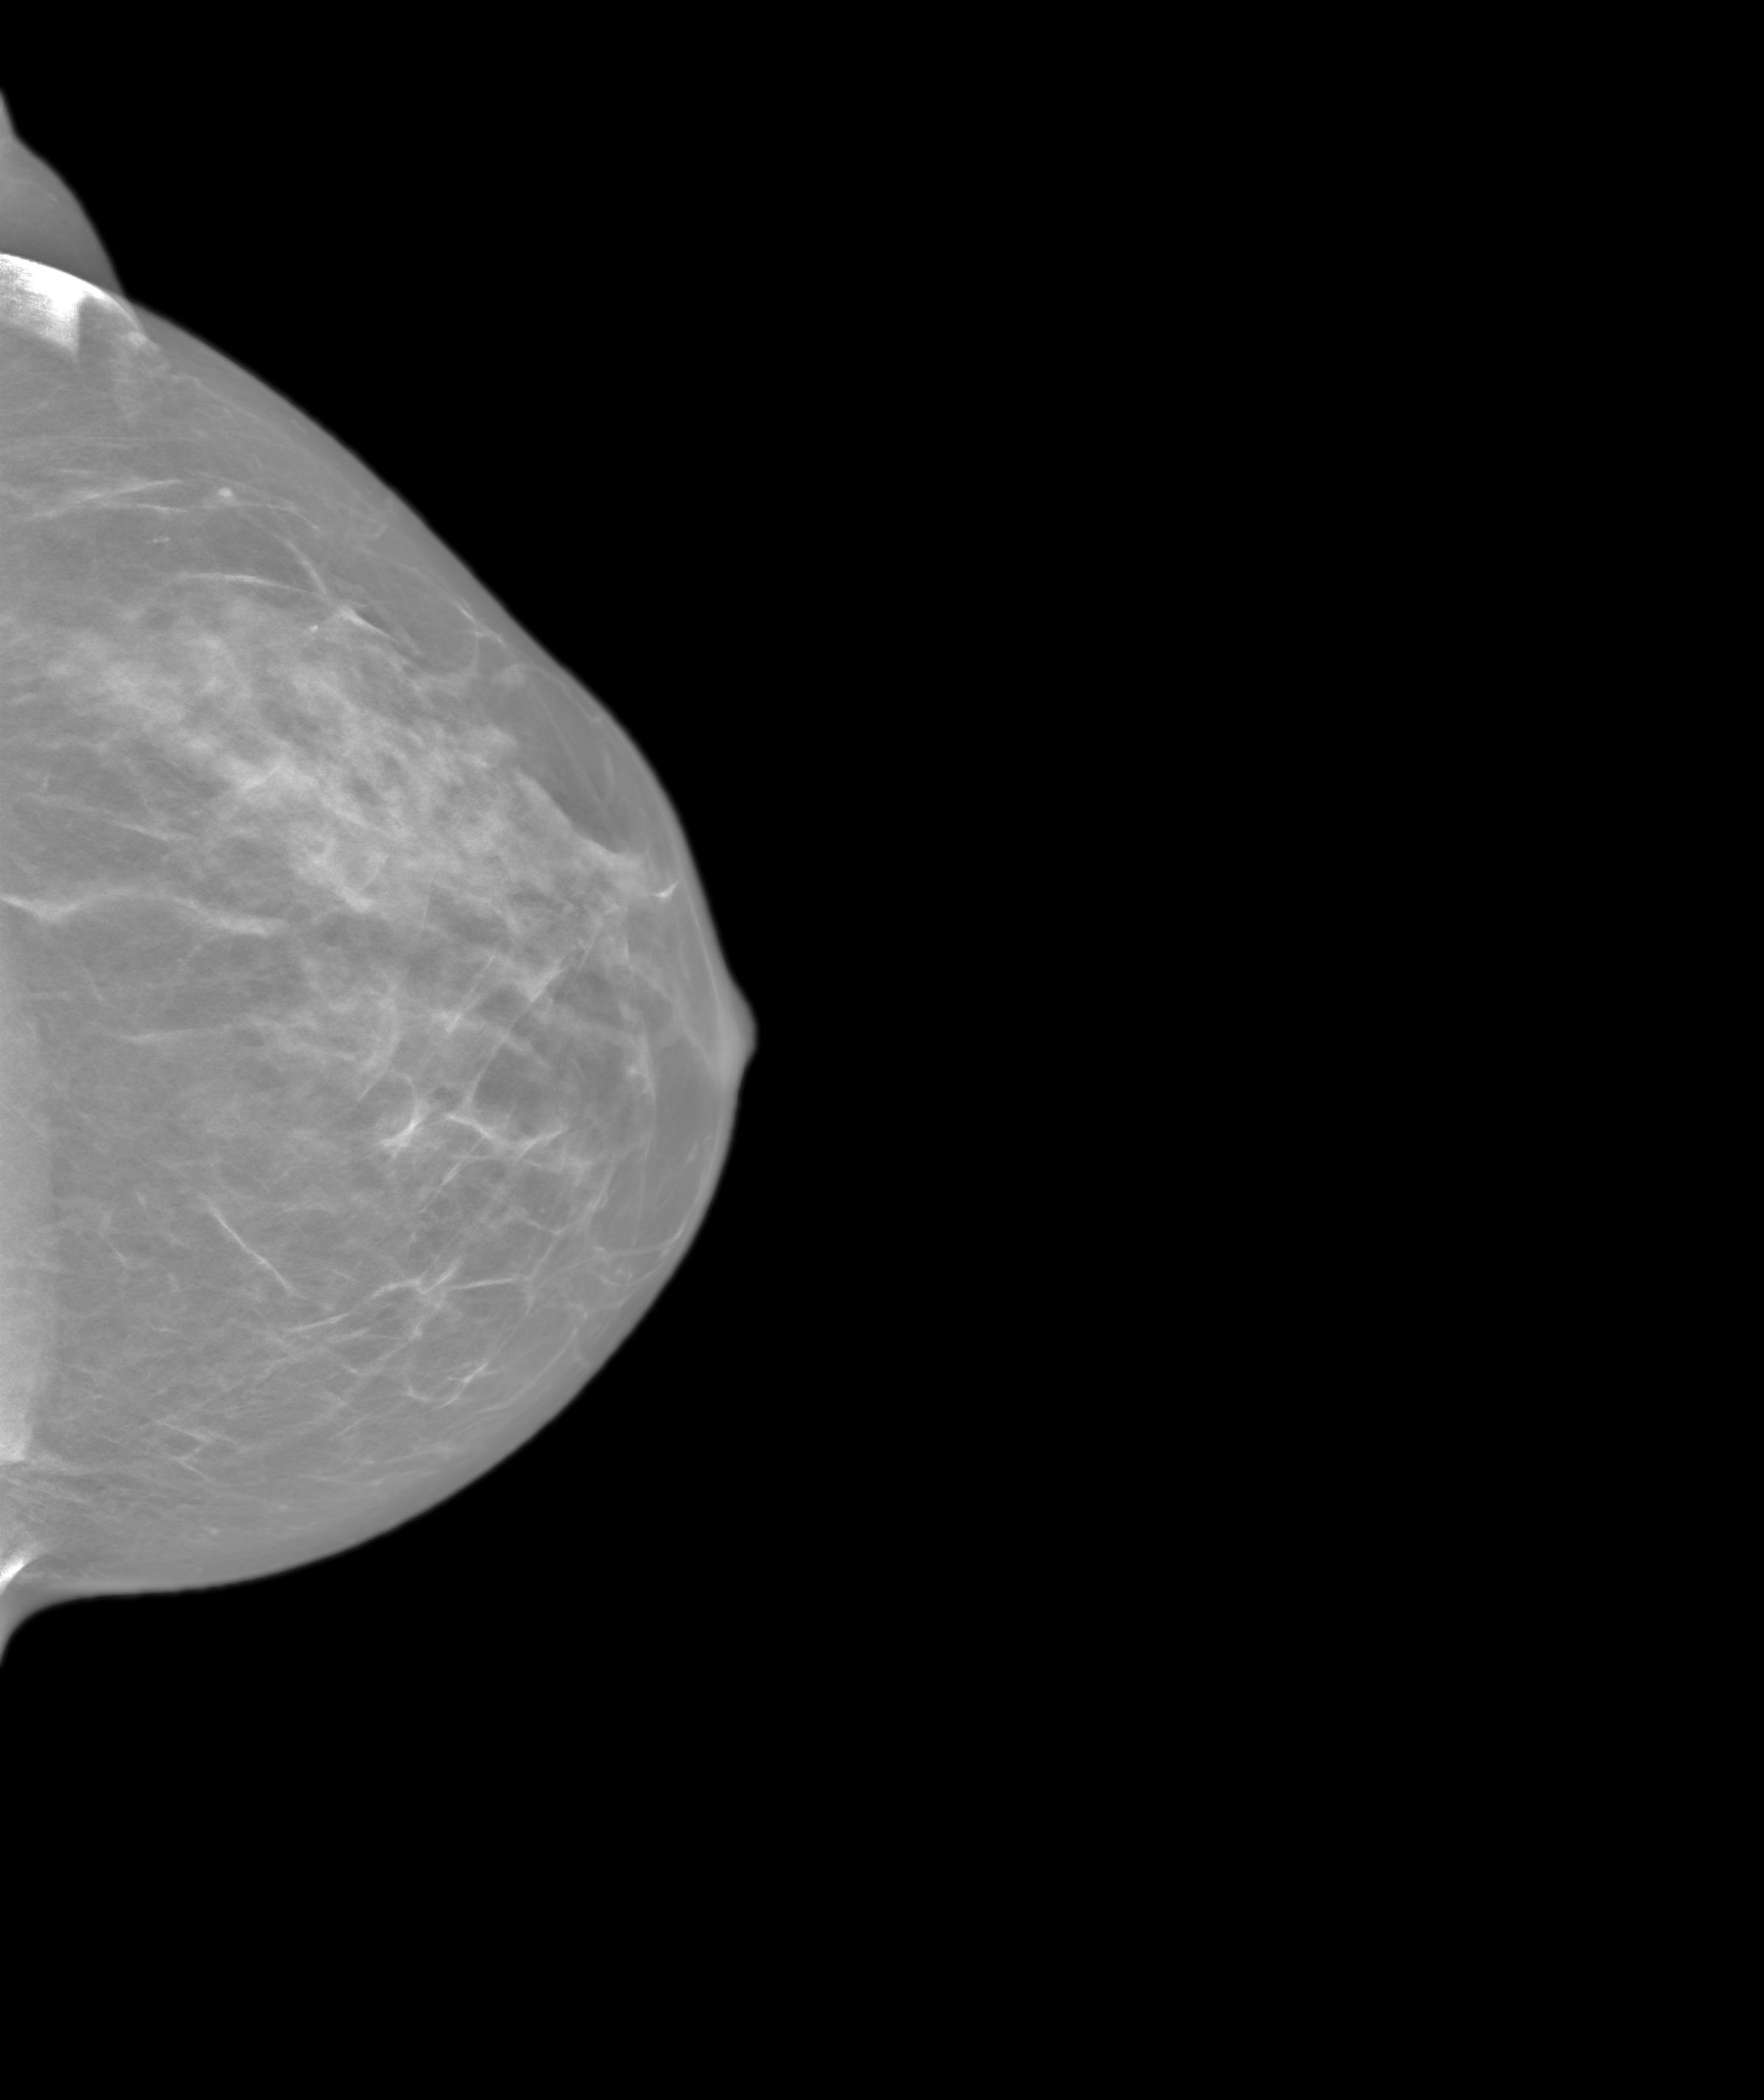
Screening examination. Patient aged 46 years (female).
Image type: synthesized 2-D view from tomosynthesis. Breast: left. Projection: cranio-caudal projection.